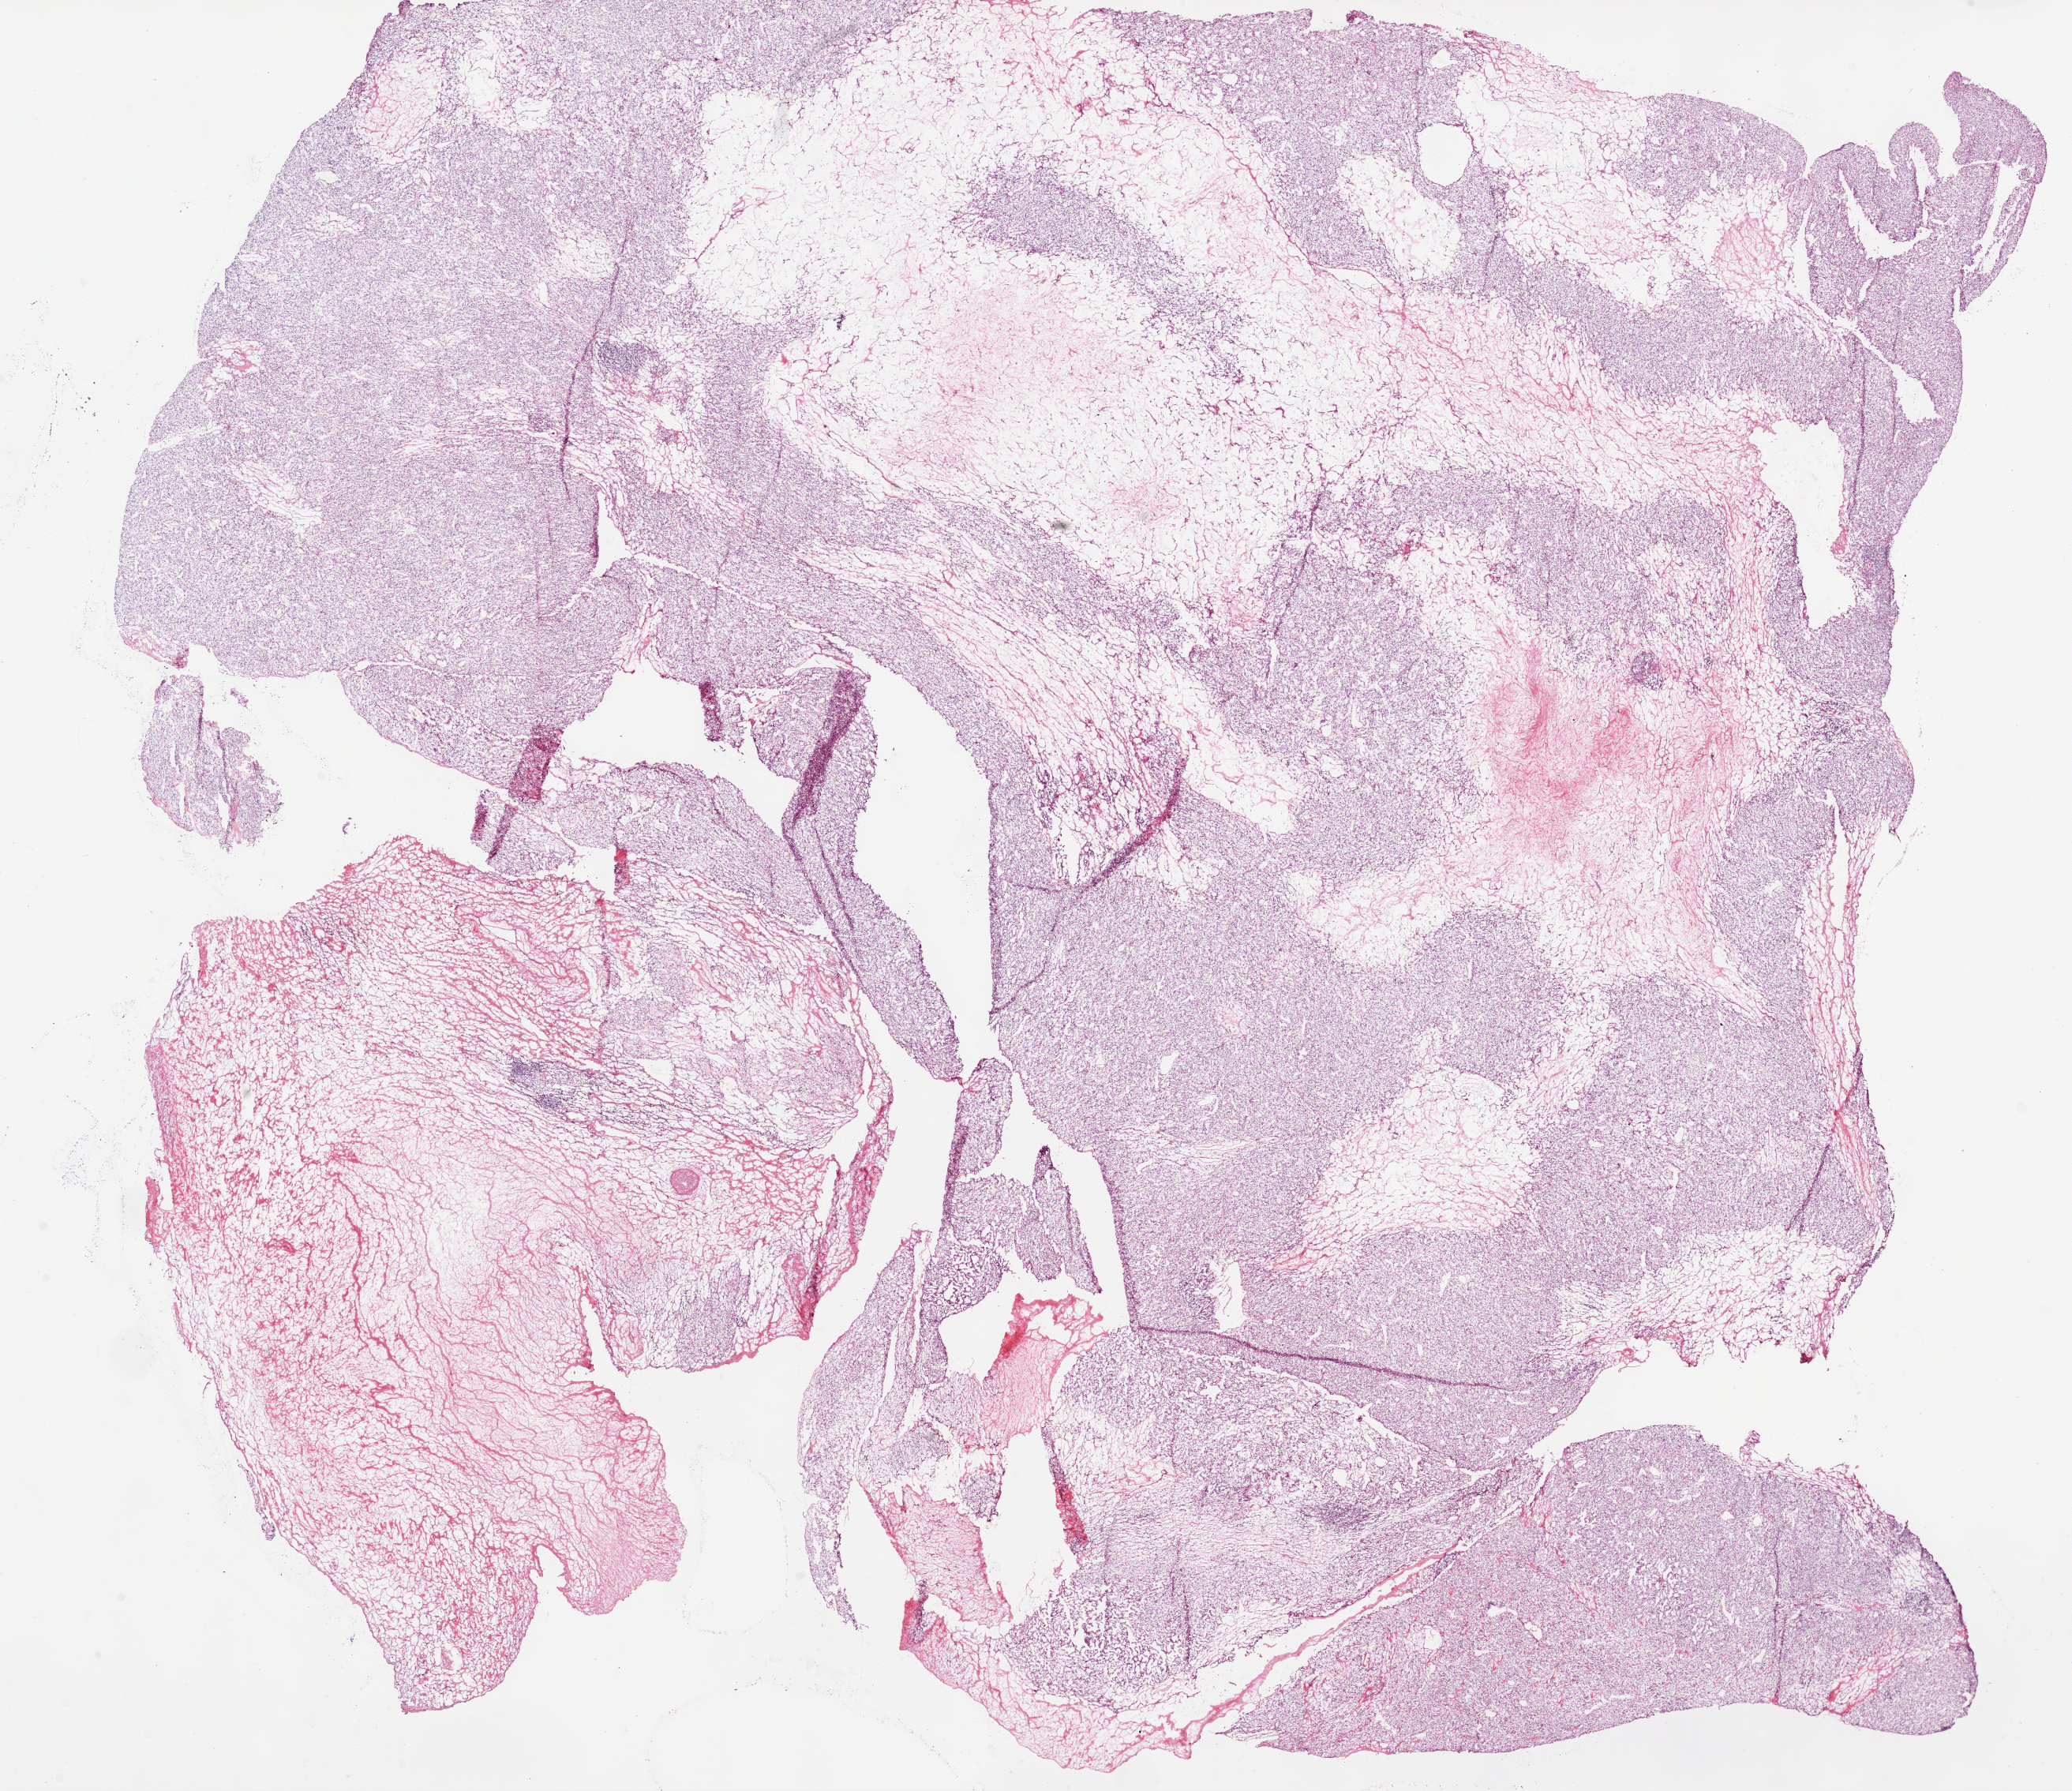
Whole-slide histology image, H&E-stained, a low-resolution overview of the entire scanned area, about 21.1 x 18.2 mm, frozen section from the bottom of the tissue portion, kidney, primary tumour sample. Female patient; age at initial diagnosis 69 years. Histologic grade: G2 (moderately differentiated). Pathologist review of this section (percent, as recorded): tumour cells 70%, tumour nuclei 80%, normal cells 0%, stromal cells 30%, necrosis 0%.
• AJCC pathologic stage: III (7th edition)
• diagnosis: Clear cell adenocarcinoma, NOS